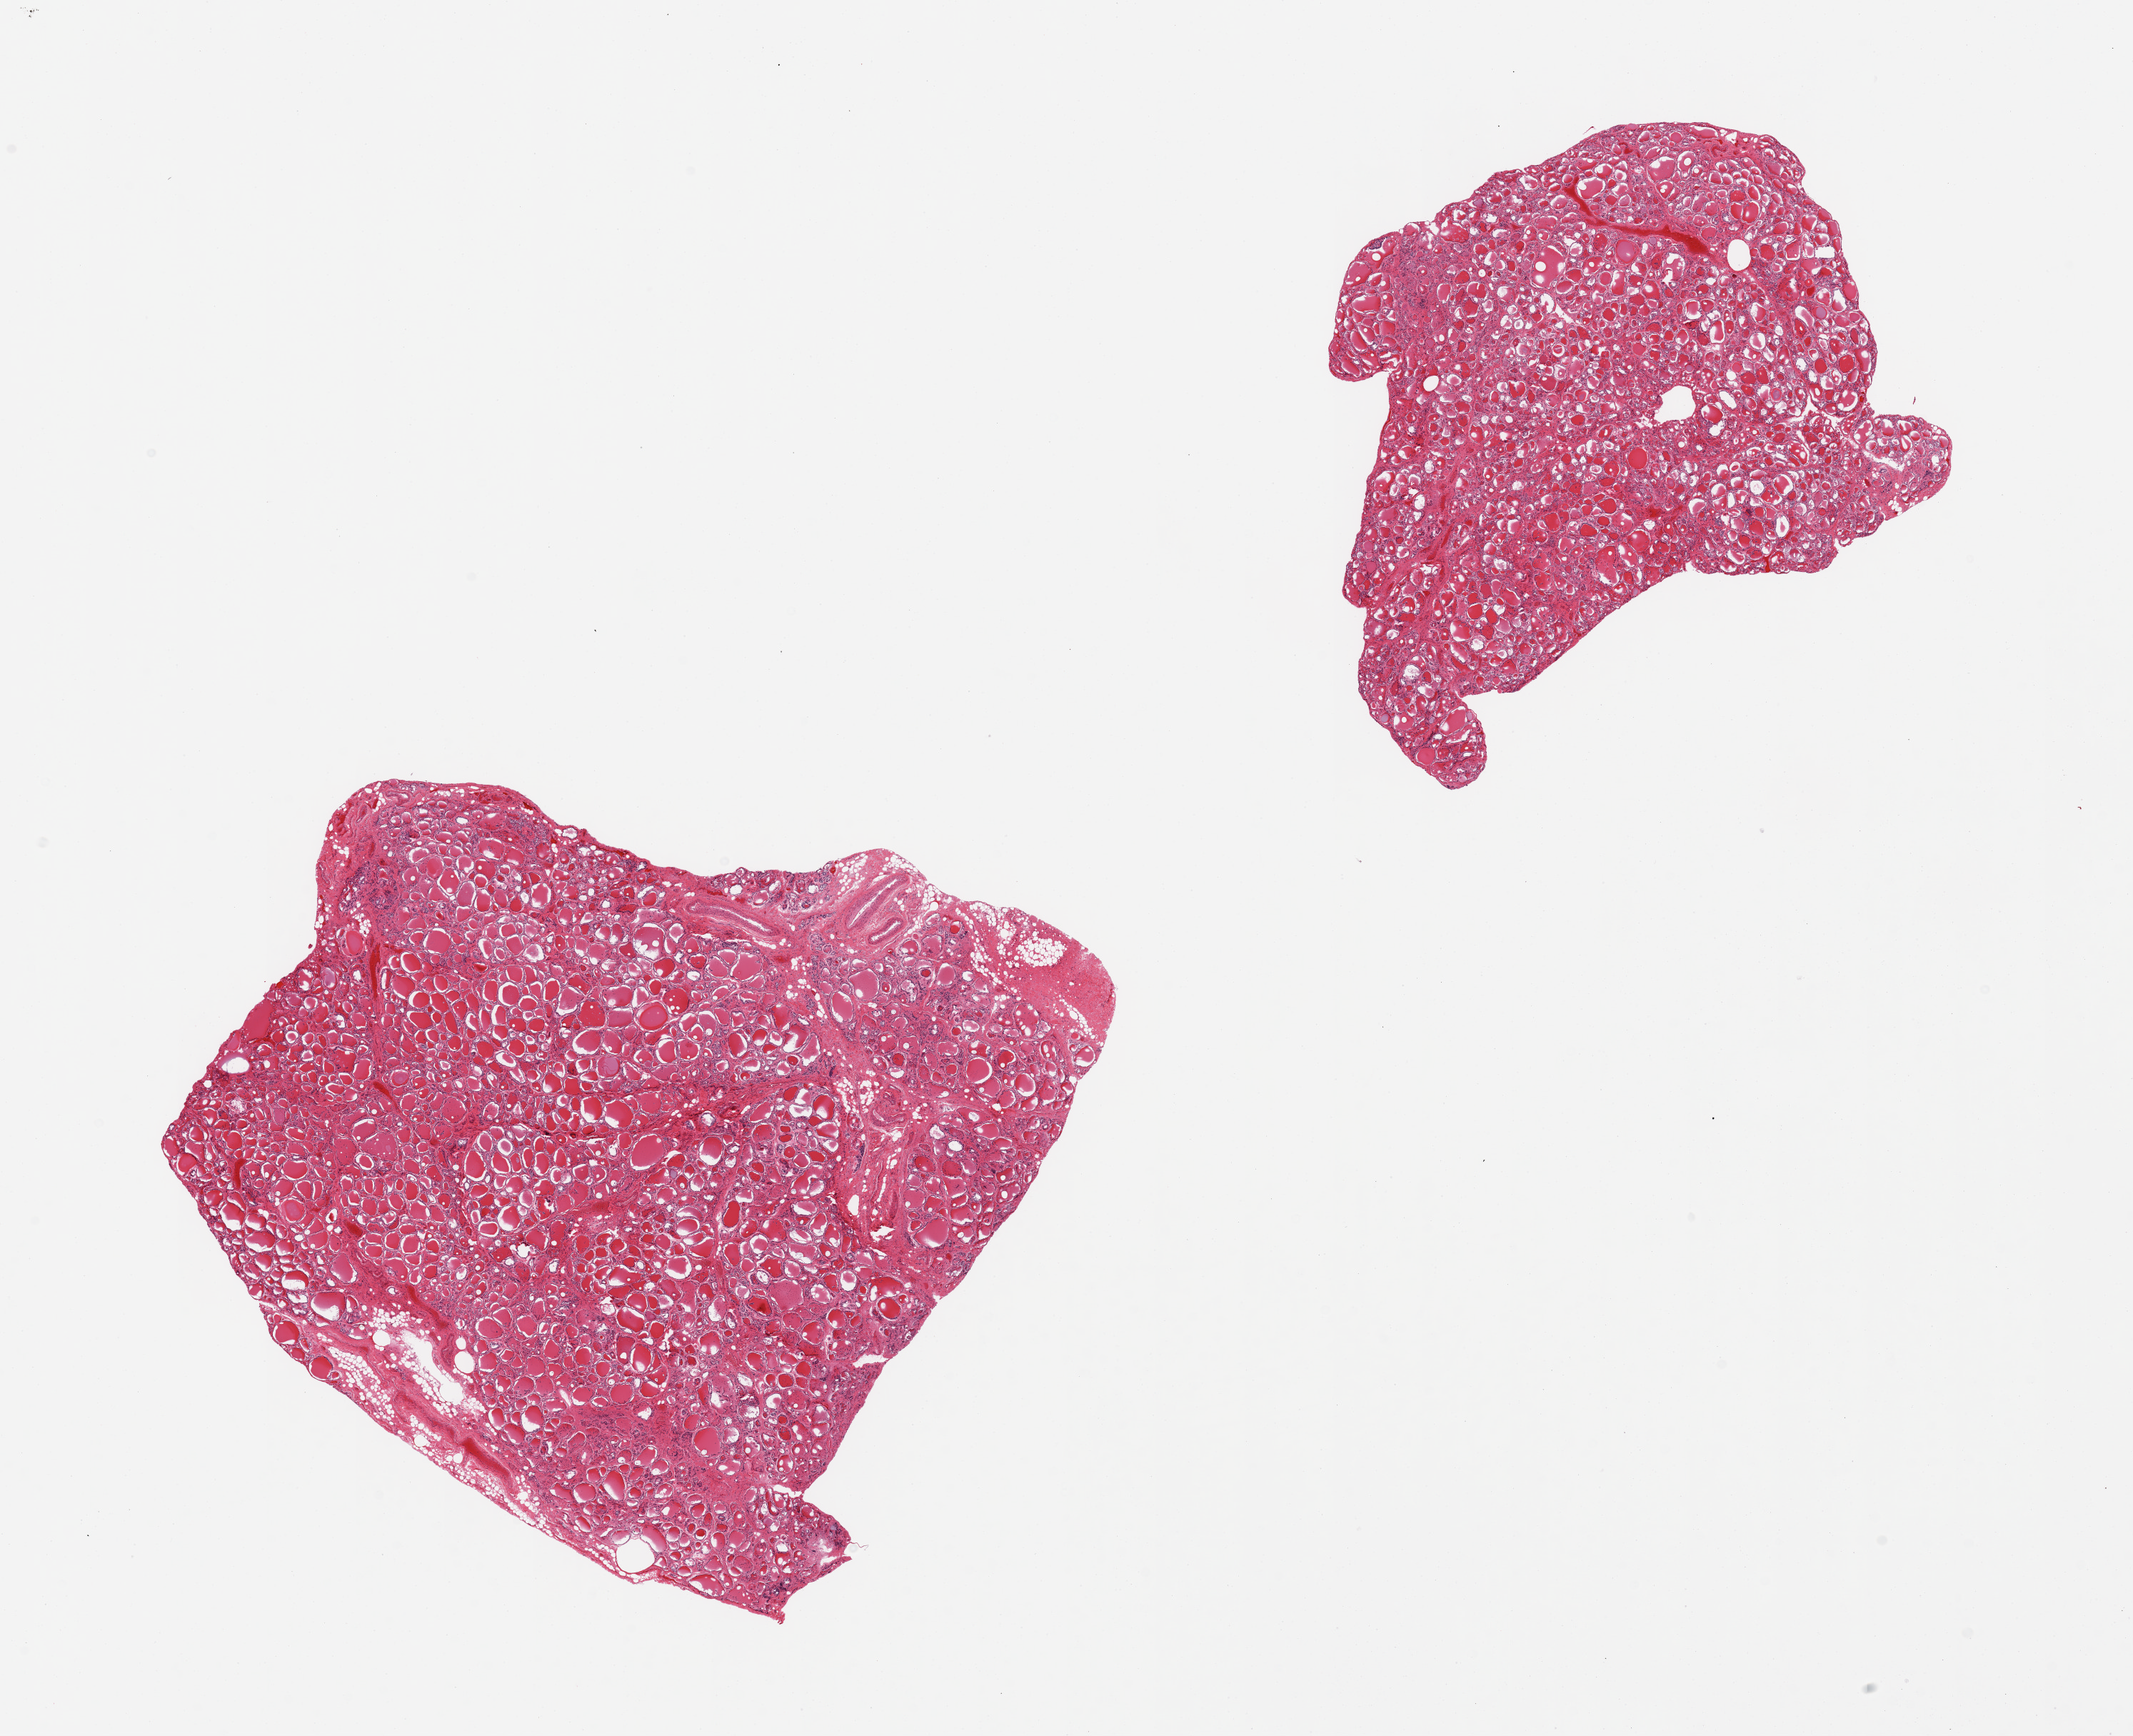
H&E whole-slide image — low-resolution overview of the scanned area, about 23.6 x 19.2 mm. PAXgene-fixed paraffin-embedded (PFPE) section. Target tissue: thyroid. Tissue donor sample.
Reviewer comment on this tissue sample: 2 pieces, no significant findings.